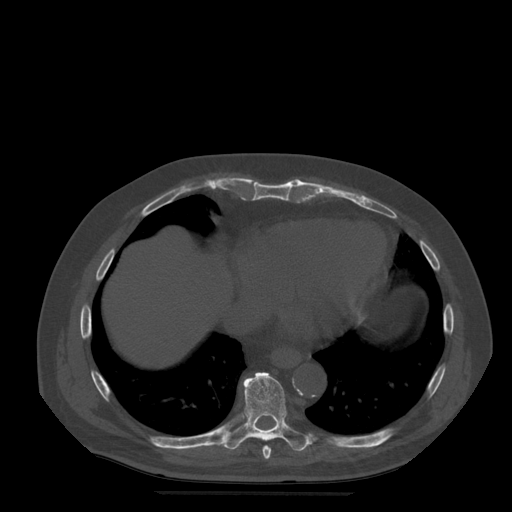
CT including the spine, one axial slice; position 294 of 522 along the scan axis; bone window (W 1800 / L 400 HU); 512 × 512 image matrix, field of view 420 × 420 mm. Patient age 72 years. Case-level facts recorded for this patient, not image findings: primary cancer: prostate.
Annotated regions visible in this slice (semi-automatic segmentation, software-assisted and operator-edited):
- T8 vertebra: bounding box [x1, y1, x2, y2] px = [263, 446, 272, 460]
- T9 vertebra: [224, 372, 310, 452]